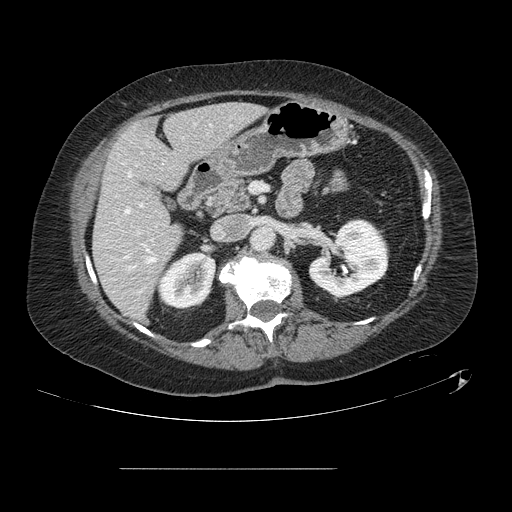
Contrast-enhanced abdominal CT, one axial slice. Slice 57 of 148 in the series (ordered by position). Soft-tissue window (W 400 / L 40 HU). 2.5 mm slice thickness. 512 × 512 image matrix, field of view 439 × 439 mm. Female patient, age 75 years. Case-level facts recorded for this patient, not image findings: diagnosis: colorectal cancer liver metastases, imaged before liver resection; multiple liver metastases: no; largest metastasis: 2.4 cm; disease in both lobes: no.
Annotated regions visible in this slice (outlined manually by an expert reader):
- hepatic veins: box from (x=125, y=173) to (x=155, y=268) px
- liver: (x=94, y=105)–(x=263, y=319)
- planned liver remnant (the part of the liver to remain after resection): (x=94, y=105)–(x=262, y=319)
- portal vein (with intrahepatic branches): (x=126, y=205)–(x=143, y=257)